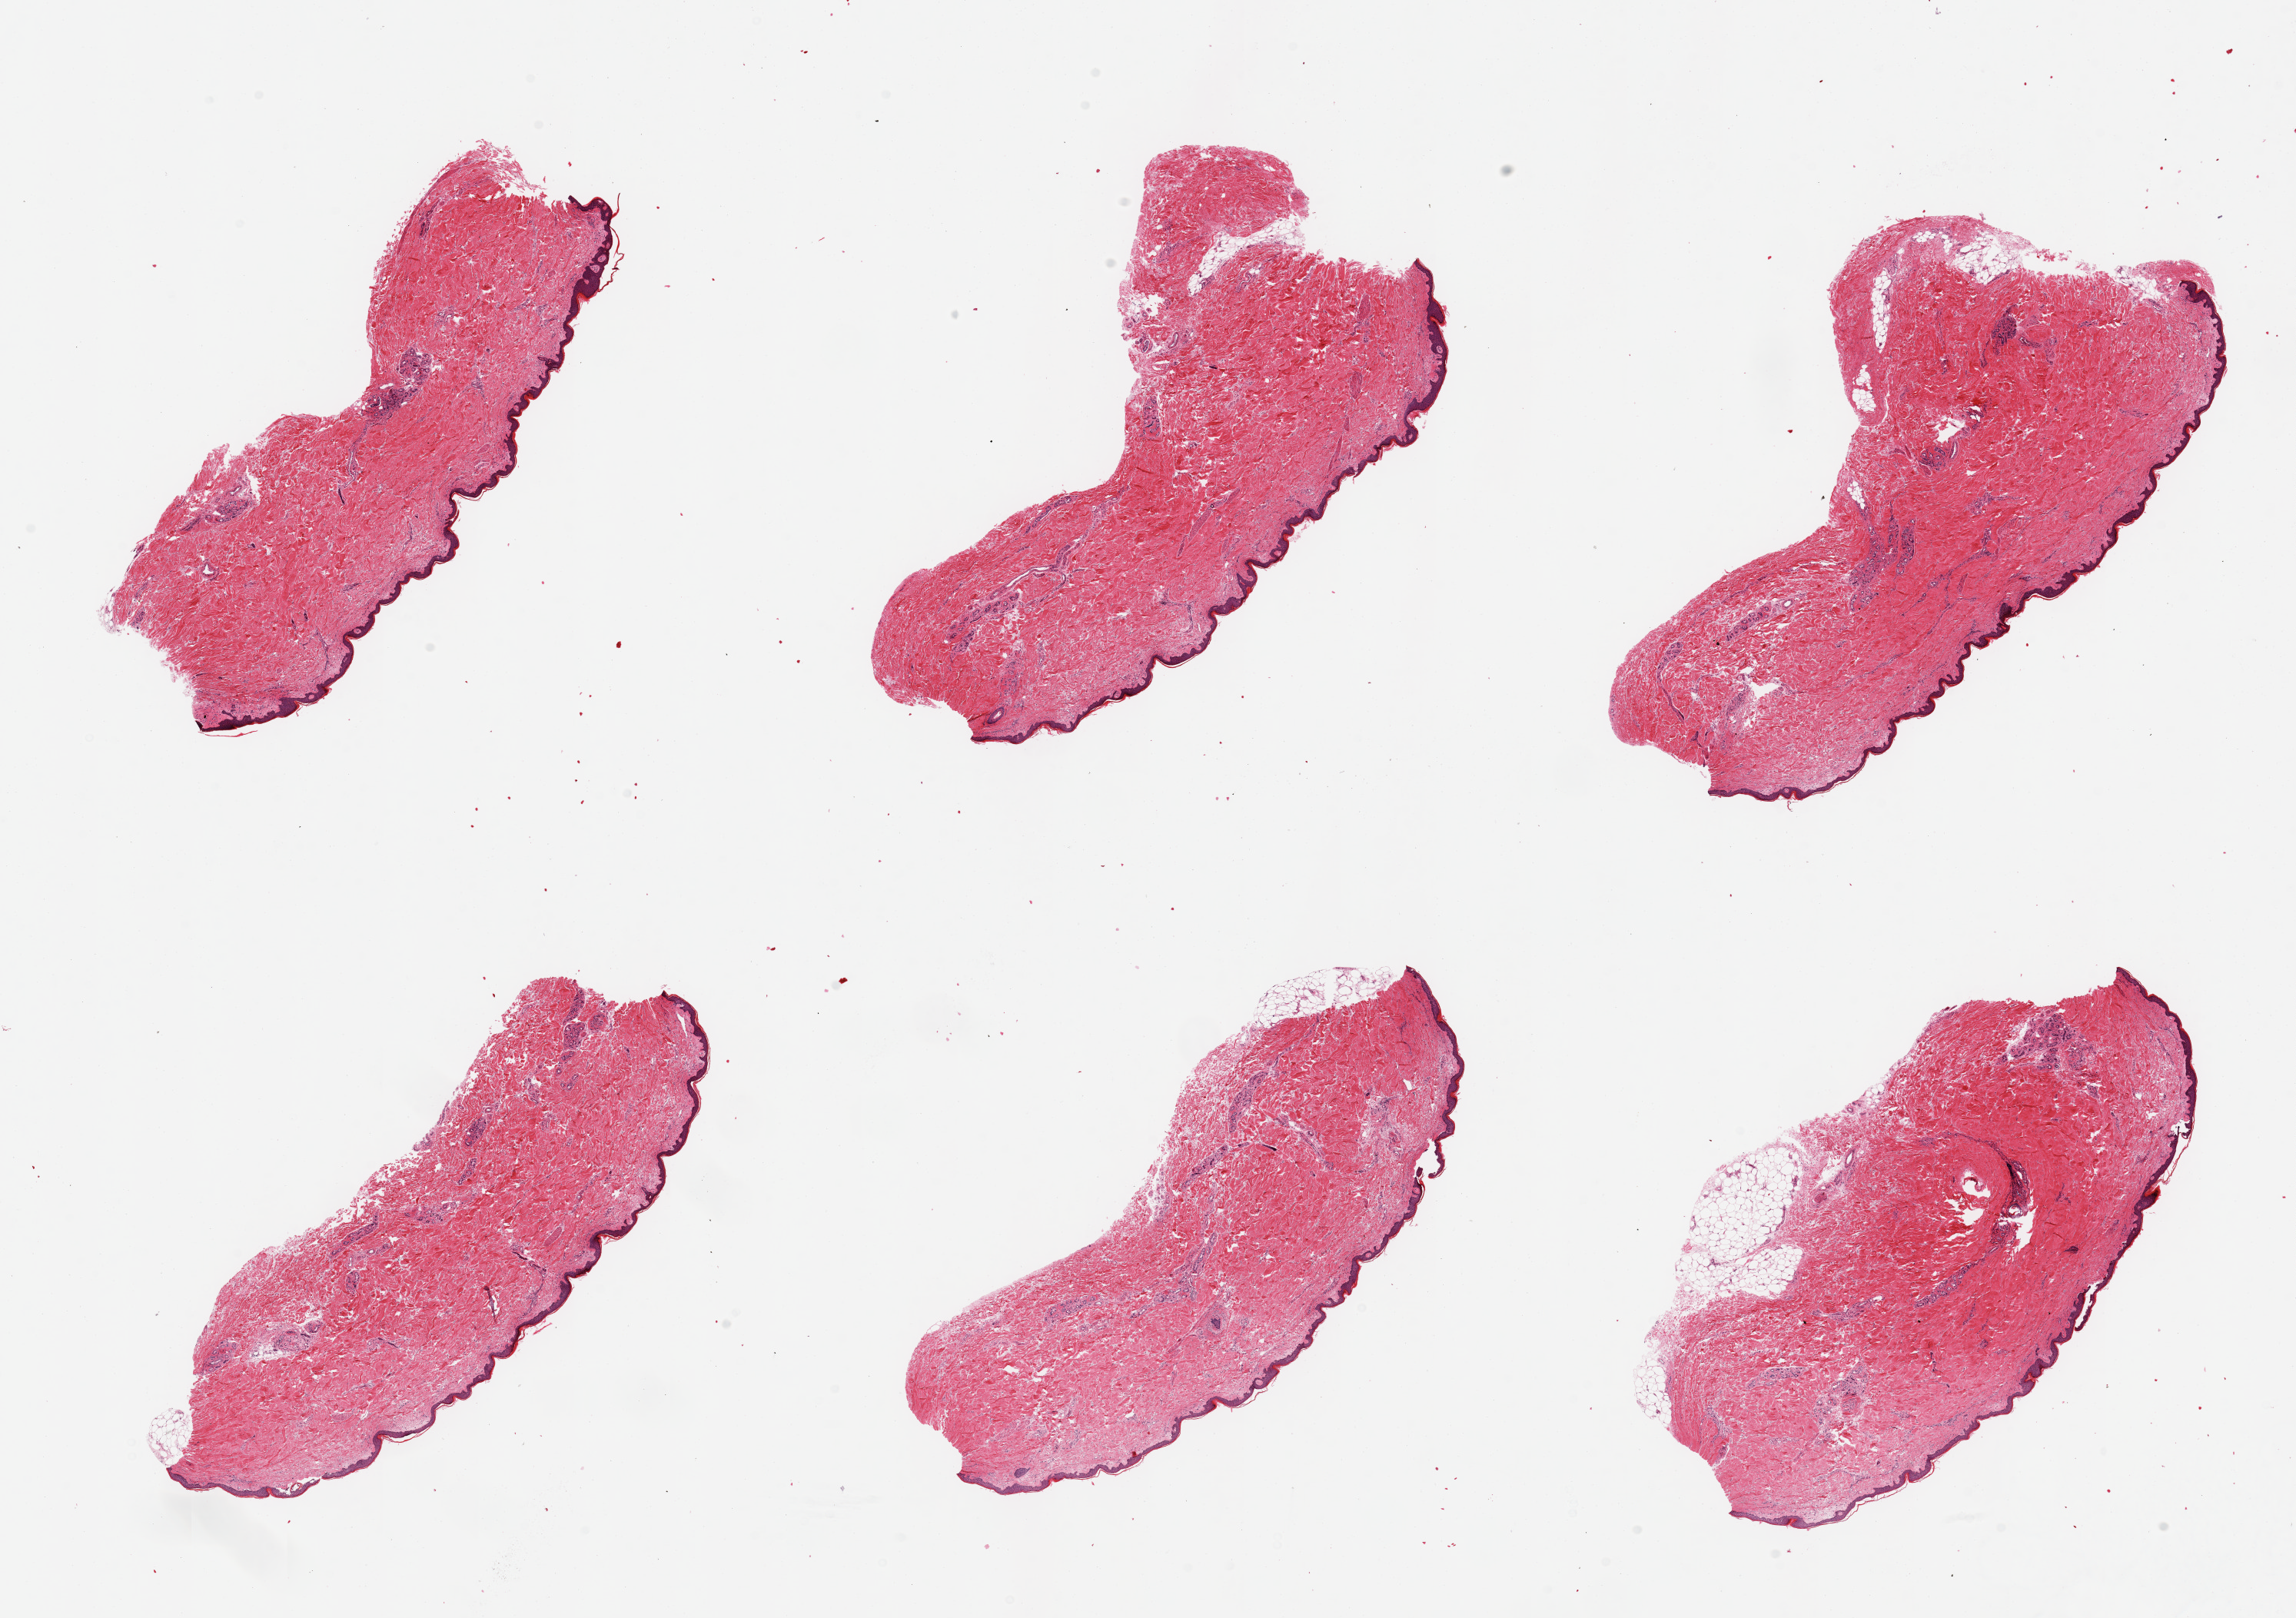
Digitized H&E-stained section, brightfield, low-resolution overview of the scanned area, about 23.6 x 16.6 mm (acquisition: 20x scan). PAXgene-fixed paraffin-embedded (PFPE) section. Target tissue: skin of lower leg. Tissue donor sample. Donor: male.
• pathologist's review note for this sample: 6 pieces; sweat glands appear atrophic; 5 of 6 pieces are well trimmed; <5% dermal fat